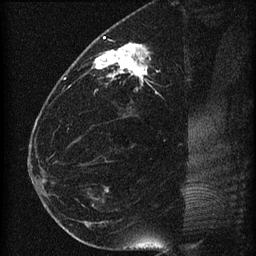
Breast MRI (dynamic contrast-enhanced), one sagittal slice; slice 29 of 60 in the series (ordered by position); dynamic contrast-enhanced series, image 2 of 4 at this slice position (ordered by acquisition); 1.5 T; TE 4.2 ms, TR 22.7 ms; 256 × 256 image matrix, field of view 180 × 180 mm. Patient: female, 35 years. Case-level facts recorded for this patient, not image findings: setting: breast cancer imaged before/during neoadjuvant chemotherapy; receptor status: HR-positive, HER2-negative.
Annotated regions visible in this slice (semi-automatic segmentation, software-assisted and operator-edited):
- analysis volume of interest (the breast-tissue region the enhancement analysis was run in; not a lesion): bounding box <69,27,198,112> (left, top, right, bottom; pixels)
- tumour enhancement mask (voxels above the 90 % enhancement threshold inside the analysis volume of interest): <93,37,148,83>